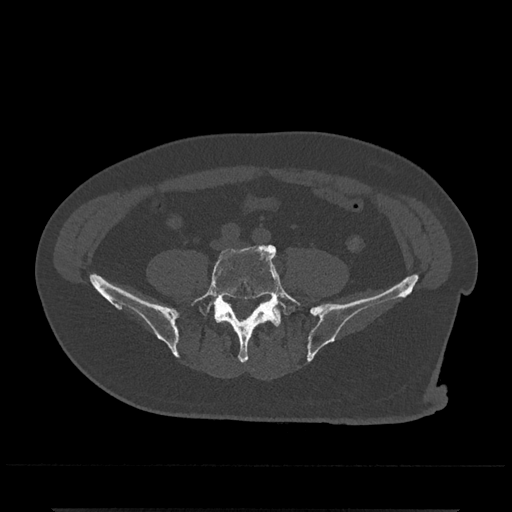
CT including the spine, one axial slice; slice 86 of 797 in the series (ordered by position); 120 kVp; bone window (W 1800 / L 400 HU); 0.5 mm slice thickness; 512 × 512 image matrix, field of view 393 × 393 mm. Male patient, age 67 years. From the clinical record (not read from this slice): primary cancer: prostate.
Structures marked on this image (semi-automatic segmentation, software-assisted and operator-edited):
- L5 vertebra: bounding box (x1, y1, x2, y2) in pixels: (188, 244, 303, 363)